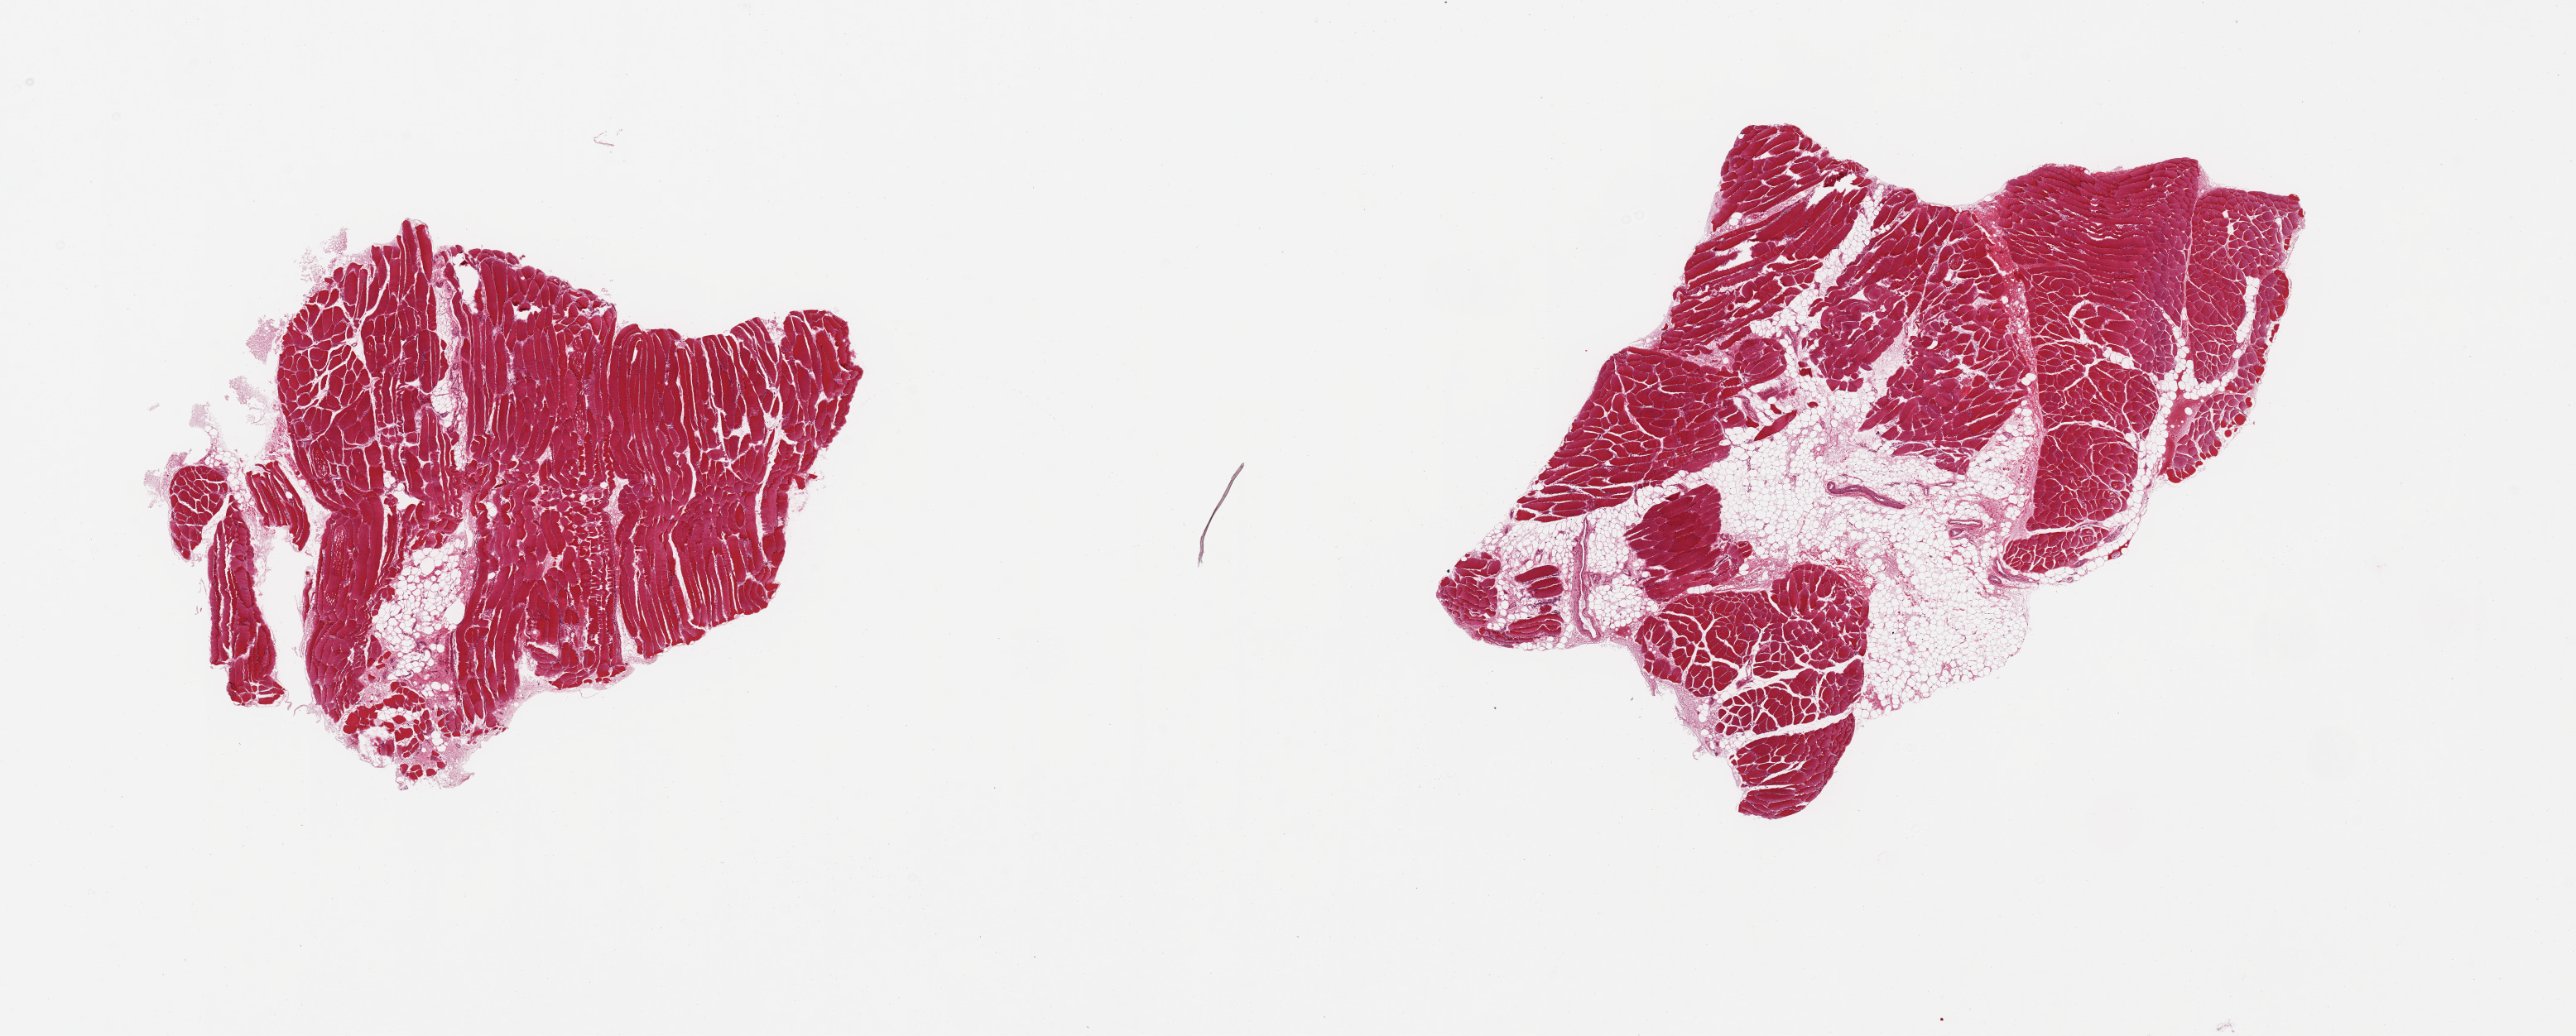
Hematoxylin and eosin (H&E) whole-slide image, low-resolution overview of the scanned area, about 24.6 x 9.9 mm (from a 20x scan); PAXgene-fixed paraffin-embedded (PFPE) section; target tissue: skeletal muscle; tissue donor sample. Donor sex: male.
Pathologist's review note for this sample: 2 pieces, interstitial fat/vascular elements ~25% specimen.